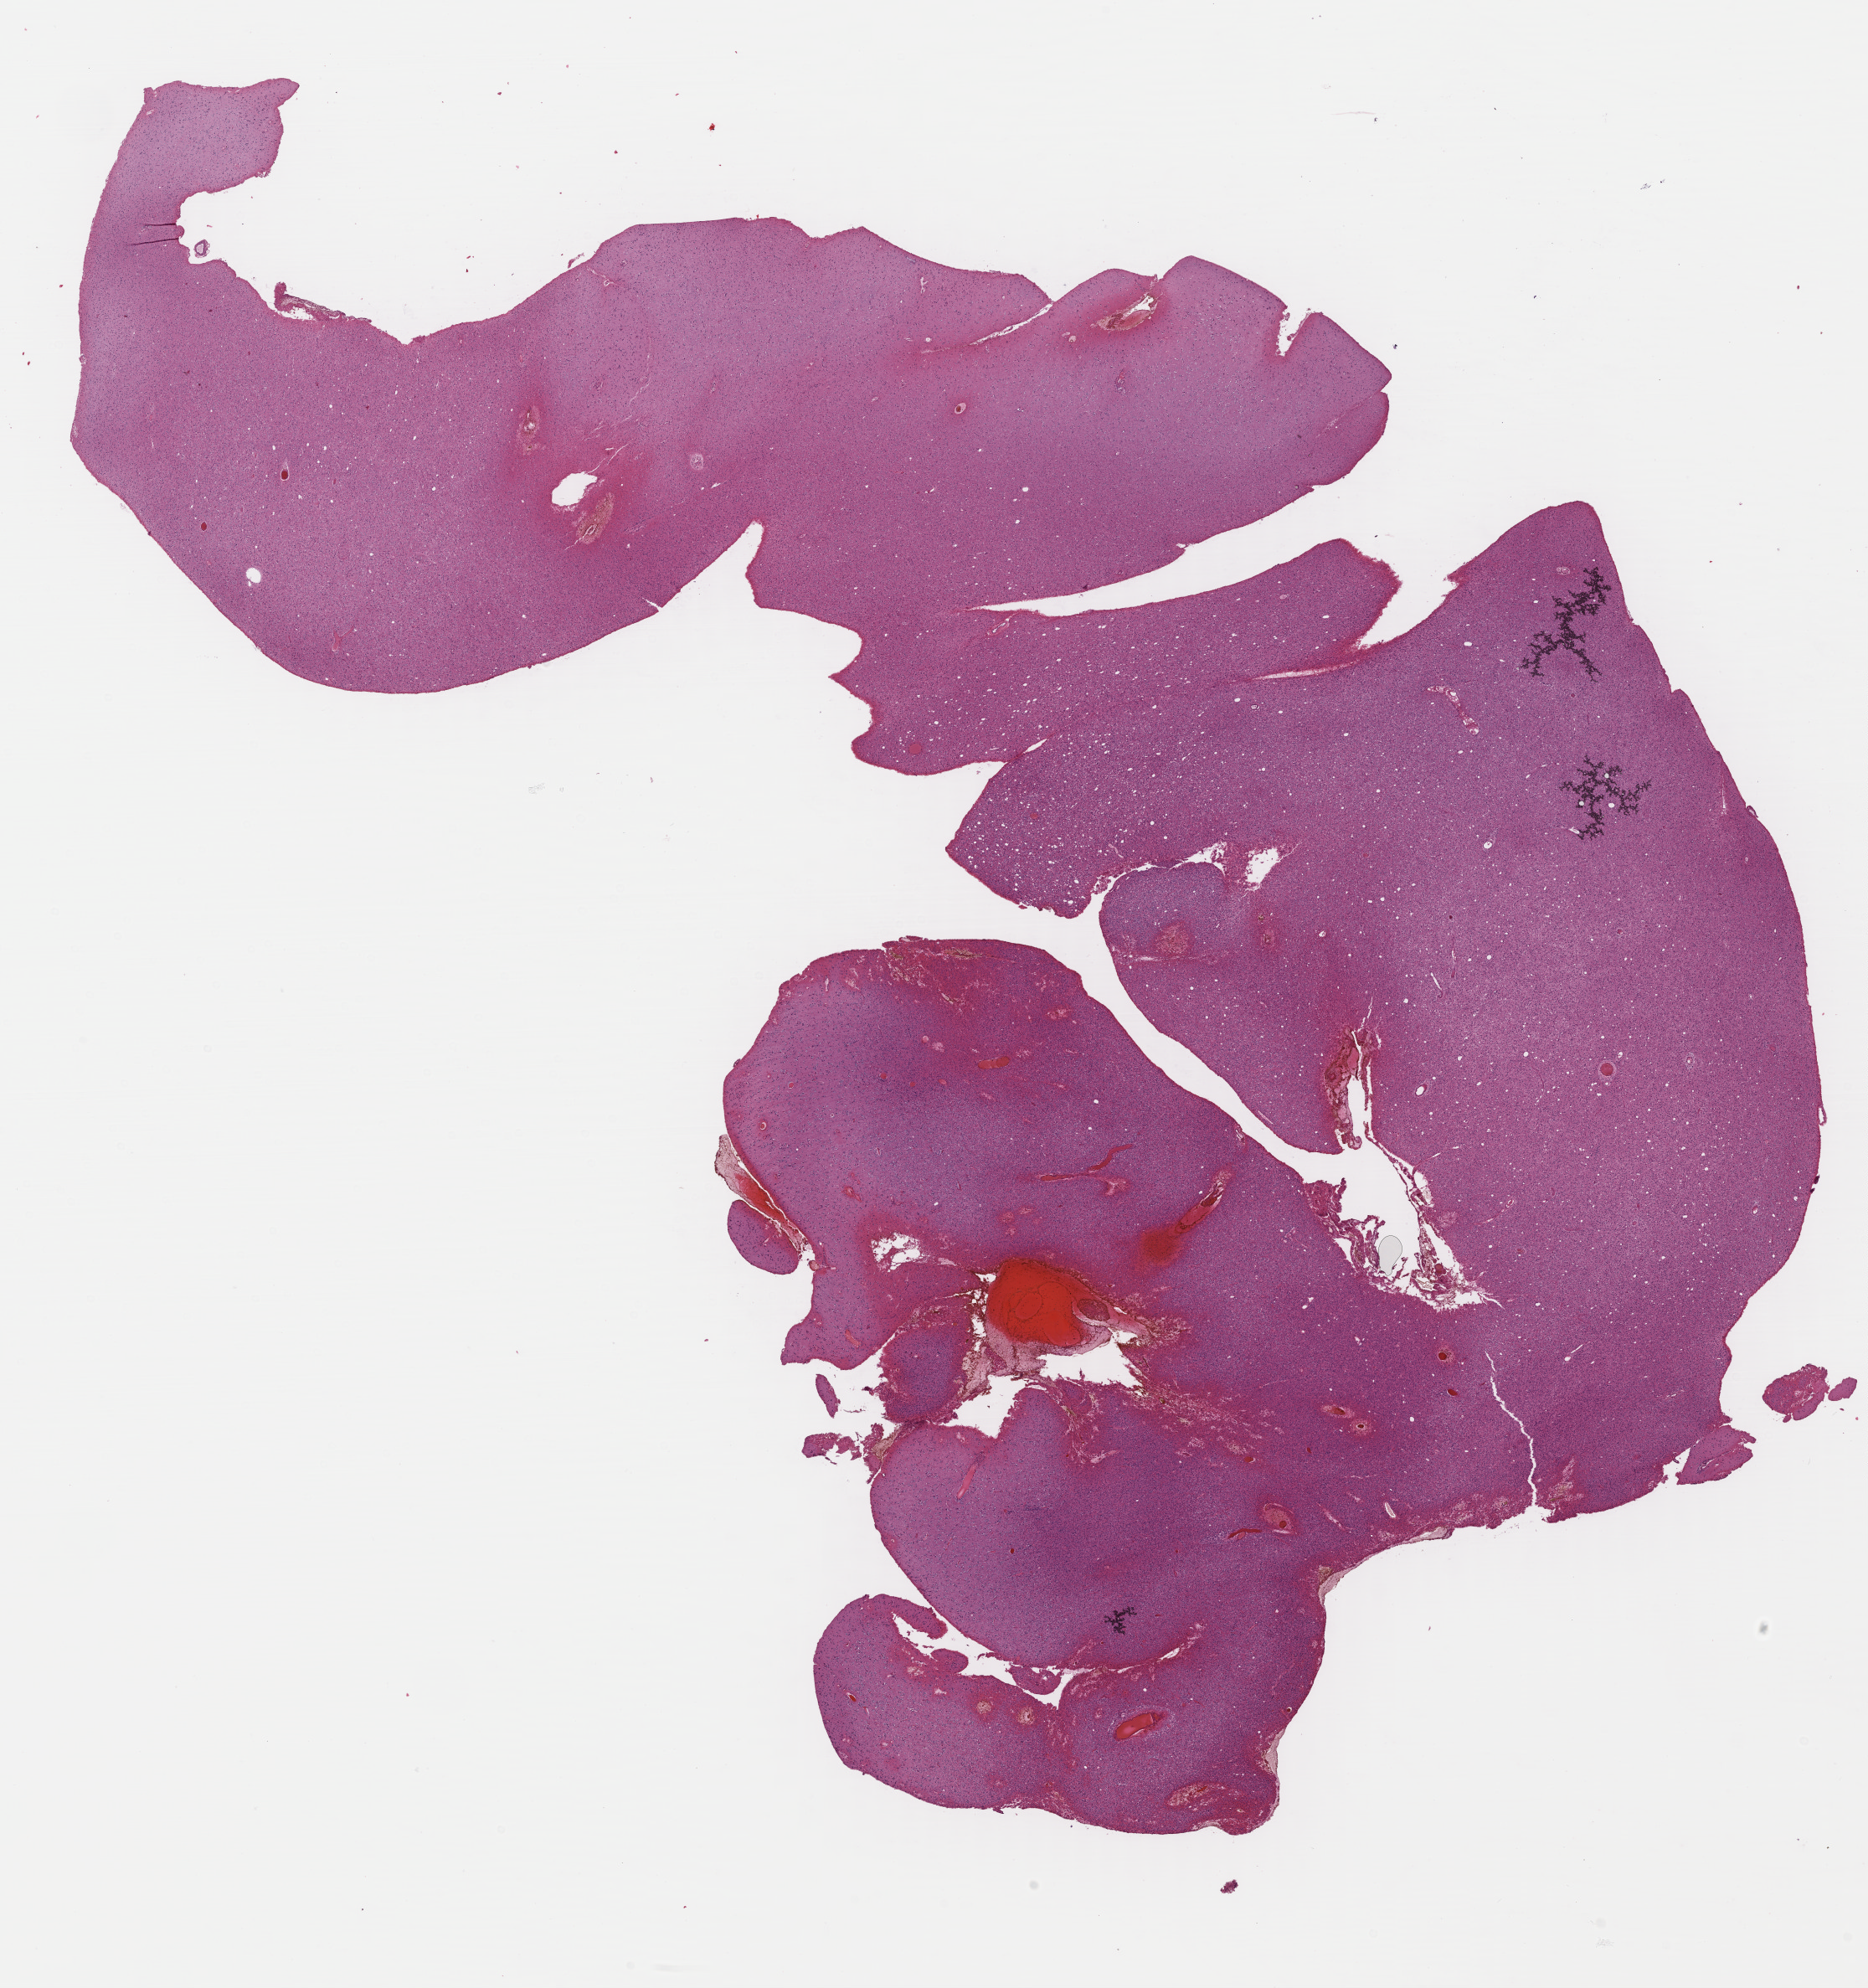
Whole-slide histology image, H&E-stained, whole scanned area (about 17.5 x 18.7 mm, from a 40x scan) shown as a low-resolution overview. Formalin-fixed paraffin-embedded (FFPE) diagnostic section. Brain, primary tumour sample. Female patient; age at initial diagnosis 20 years. Histologic grade: G2 (moderately differentiated).
Histologic diagnosis: Oligodendroglioma, NOS.